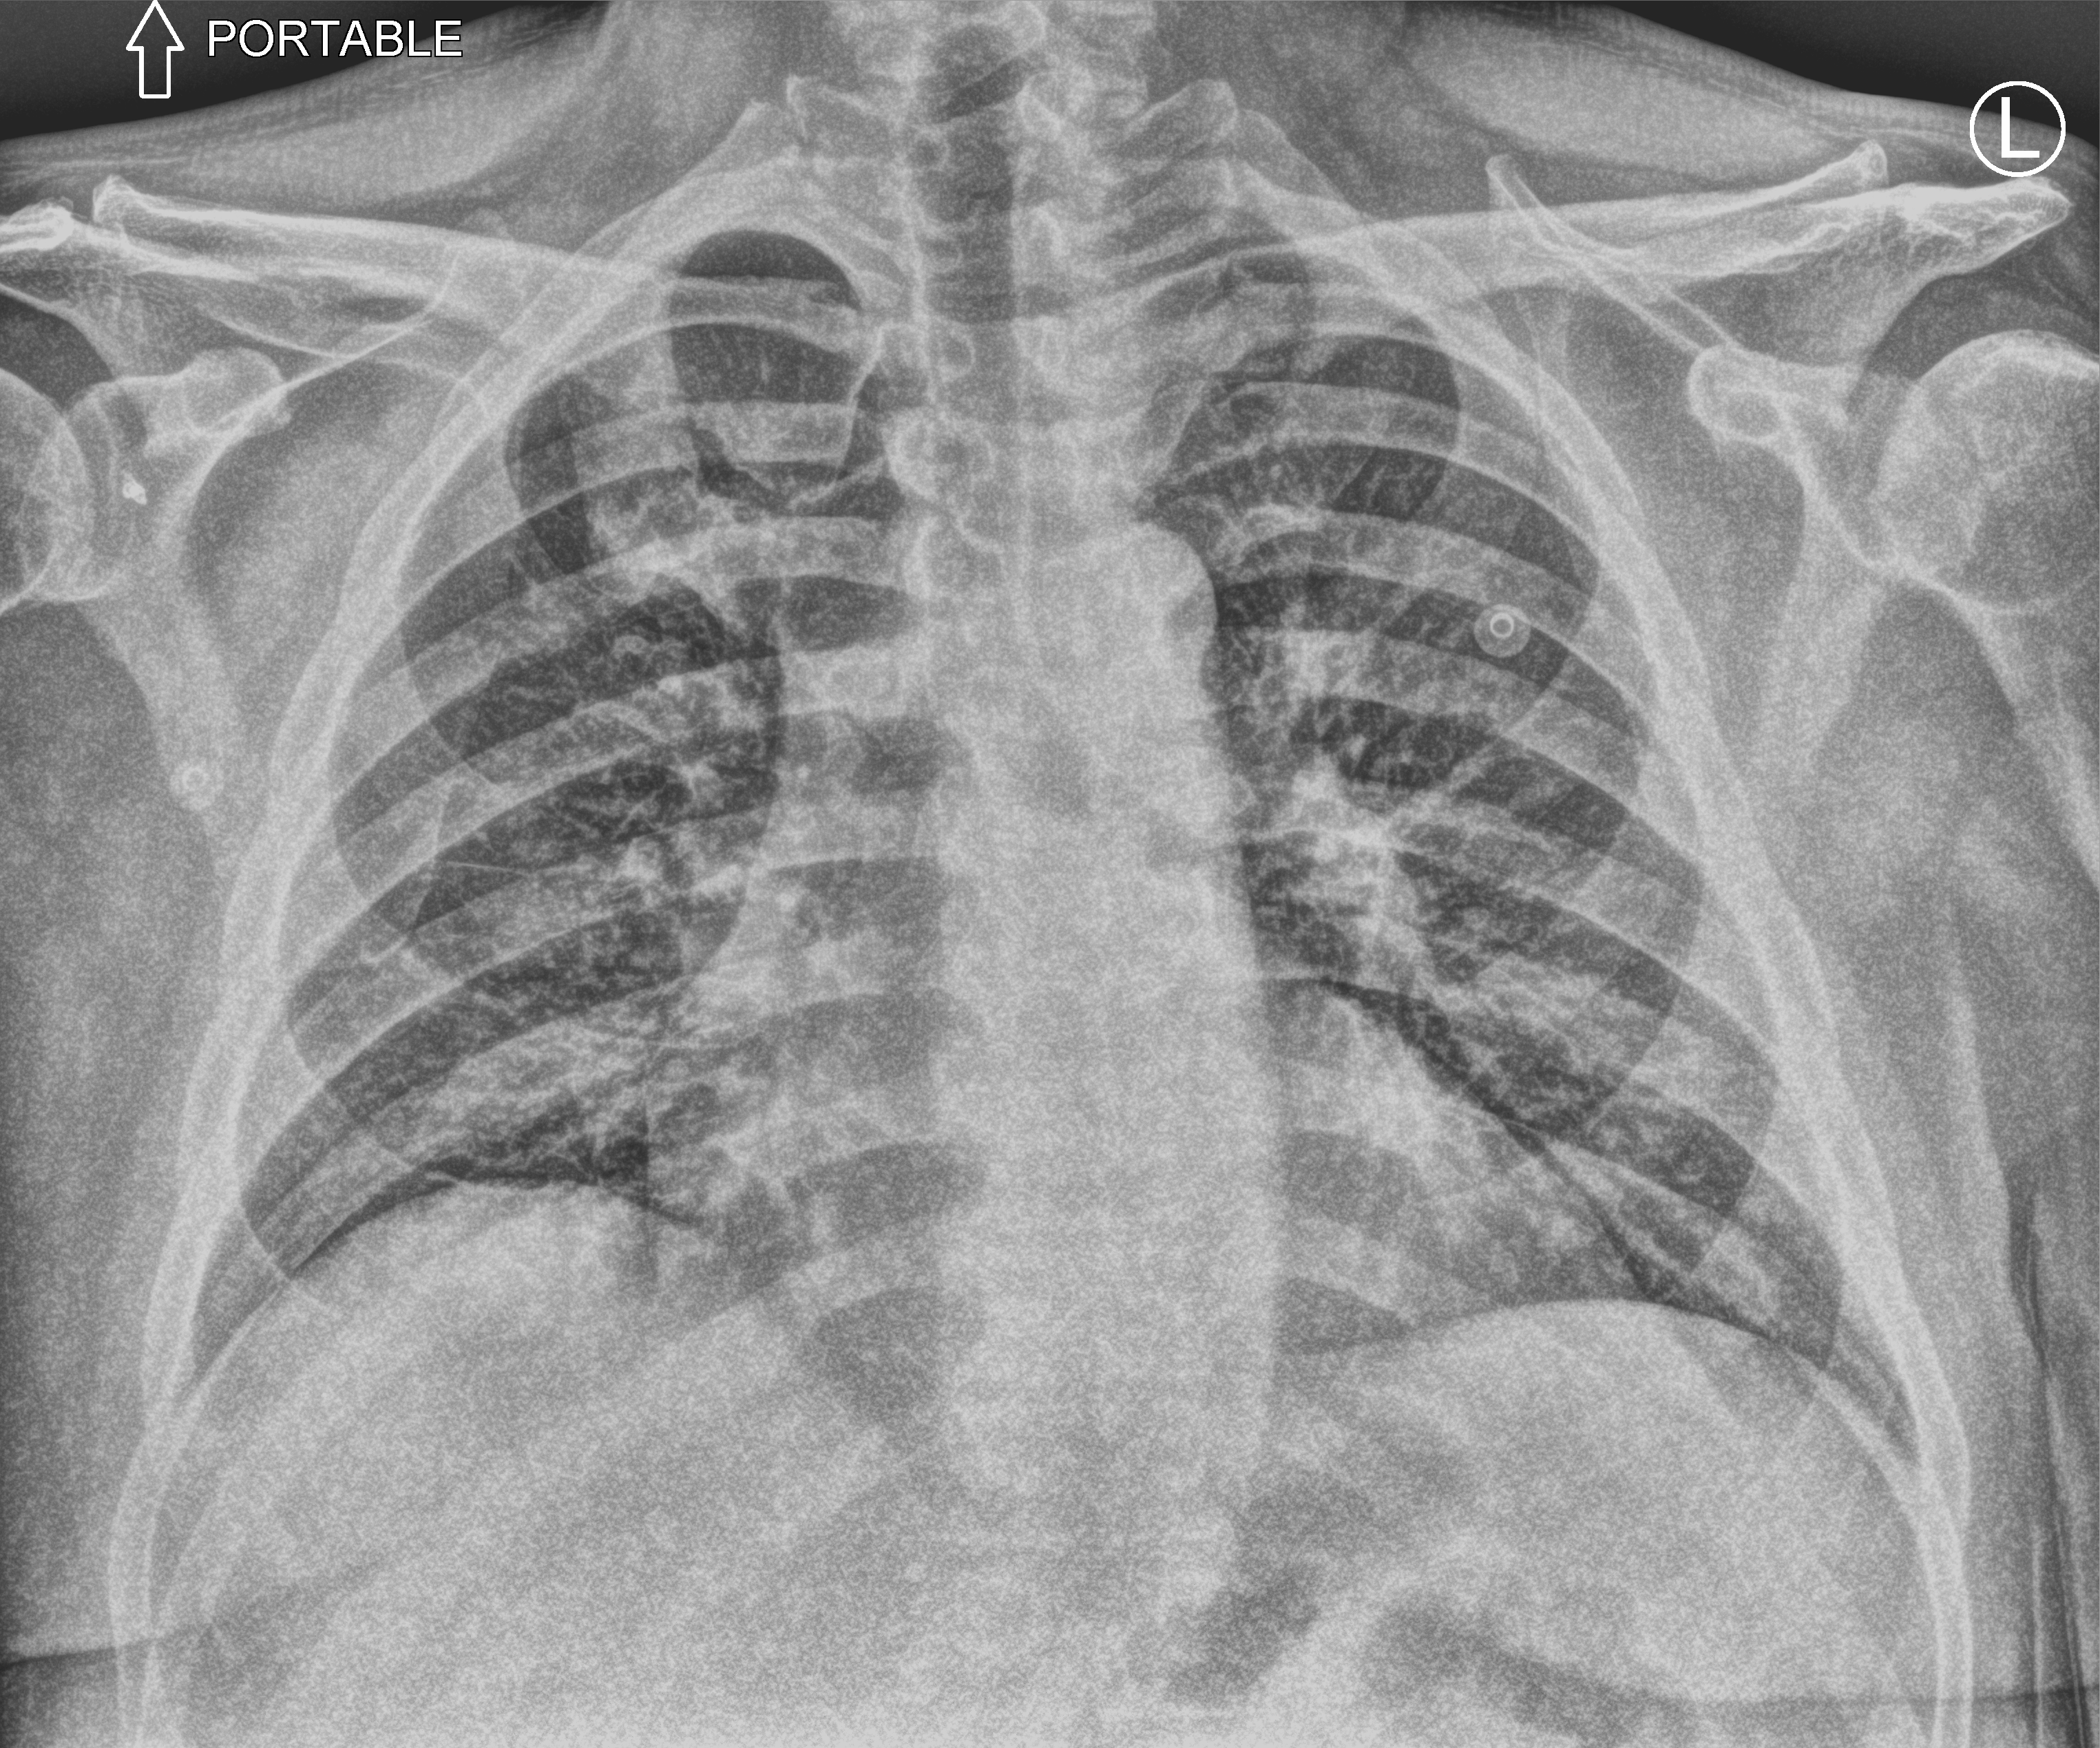
Chest X-ray (portable), anteroposterior (AP) projection. Male patient hospitalised with COVID-19, age 18–59 years.
Hospital-stay facts (about this admission, not read from this image; timing relative to this image not recorded): other chronic lung disease (admission record): yes.